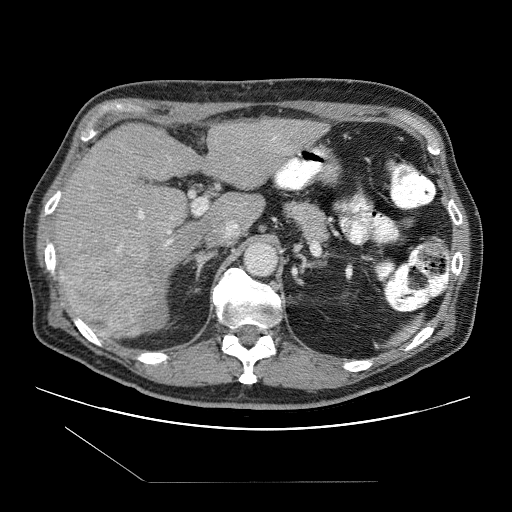
Contrast-enhanced abdominal CT (liver protocol), one axial slice. Slice 59 of 109 in the series (ordered by position). Reconstruction kernel STANDARD. One of 2 acquisitions stored at this slice position. Soft-tissue window (W 400 / L 40 HU). 2.5 mm slice thickness. 512 × 512 image matrix, field of view 400 × 400 mm. Case-level facts recorded for this patient, not image findings: diagnosis: hepatocellular carcinoma (patient treated with transarterial chemoembolisation; whether this scan precedes or follows treatment is not stated here); TNM stage (as recorded): Stage-IIIB; Child-Pugh class: A; tumour nodularity: multinodular.
Outlined on this slice (semi-automatic segmentation, software-assisted and operator-edited):
- liver parenchyma outside the tumour (the mass and vessels are separate outlines, so this box may not span the whole liver): bounding box <54,118,326,336> (left, top, right, bottom; pixels)
- mass: <59,232,155,337>
- liver vessels: <138,137,276,244>